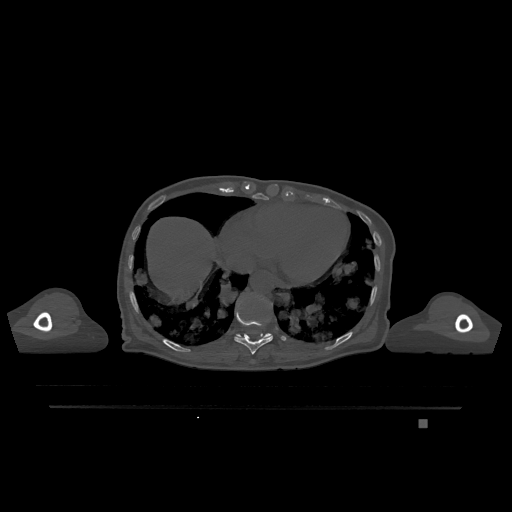
CT including the spine, one axial slice; position 628 of 1317 along the scan axis; bone window (W 1800 / L 400 HU); 512 × 512 image matrix. Patient: female, 74 years. Case-level facts recorded for this patient, not image findings: primary cancer: lung; vertebrae with lytic lesions (as recorded): T1, T4, T5, T6, L4, L5.
Structures marked on this image (semi-automatic segmentation, software-assisted and operator-edited):
- T10 vertebra: bounding box [x1, y1, x2, y2] px = [234, 311, 273, 354]
- T11 vertebra: [237, 333, 271, 338]